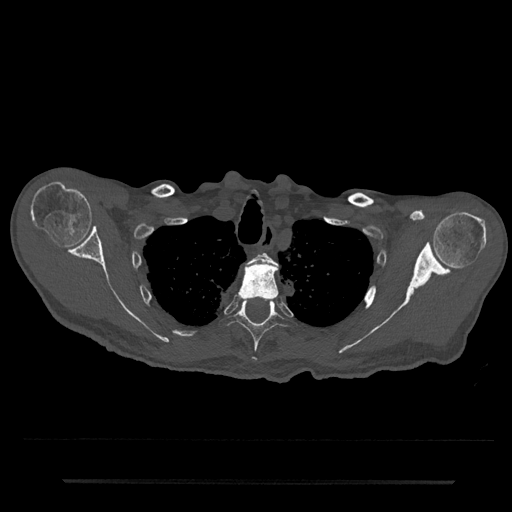
CT including the spine, one axial slice; slice 638 of 797 in the series (ordered by position); reconstruction kernel Br40s/3; 120 kVp; bone window (W 1800 / L 400 HU); 0.5 mm slice thickness; 512 × 512 image matrix, field of view 427 × 427 mm. Patient: male, 74 years. From the clinical record (not read from this slice): primary cancer: prostate.
Structures marked on this image (semi-automatic segmentation, software-assisted and operator-edited):
- T2 vertebra: bounding box [x1, y1, x2, y2] px = [250, 253, 276, 265]
- T3 vertebra: [238, 261, 279, 301]
- T4 vertebra: [225, 299, 287, 362]